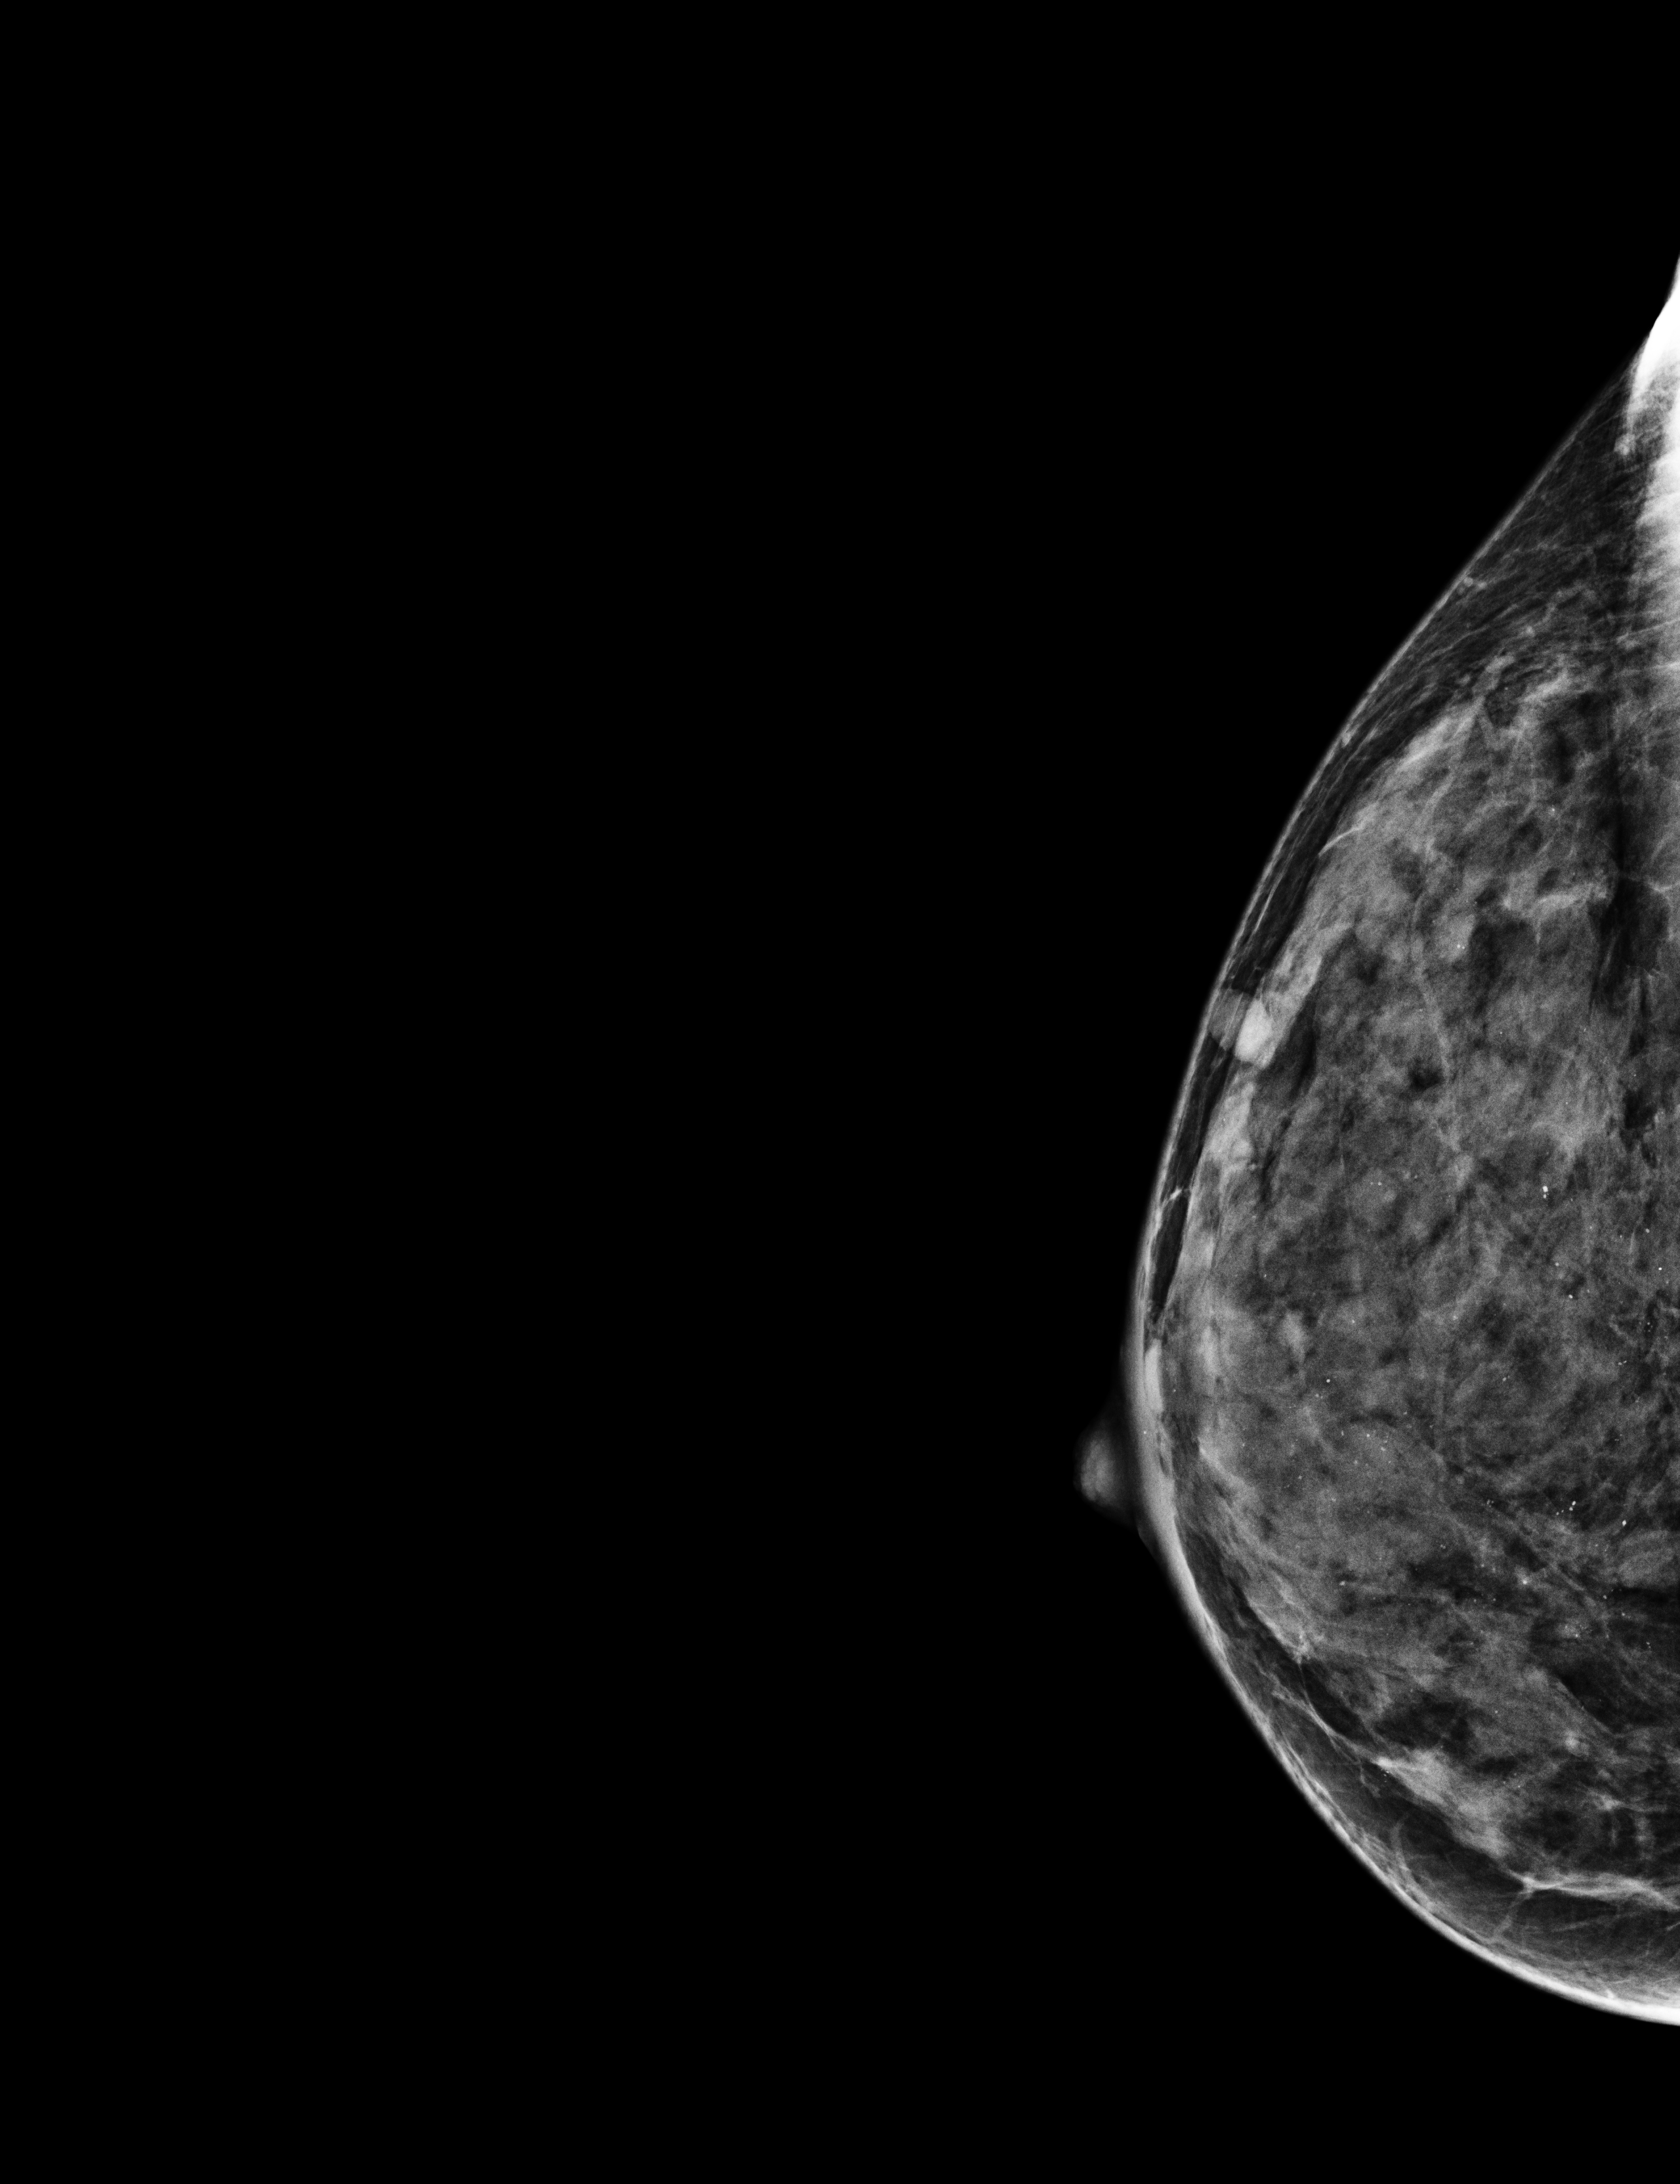
Full-field digital mammogram (FFDM); right breast; laterally exaggerated craniocaudal (XCCL) view; annual screening mammography examination; system: Selenia Dimensions. Patient: female, 49 years.
BI-RADS breast density category at the screening exam (both breasts, scale 1–4): 4.